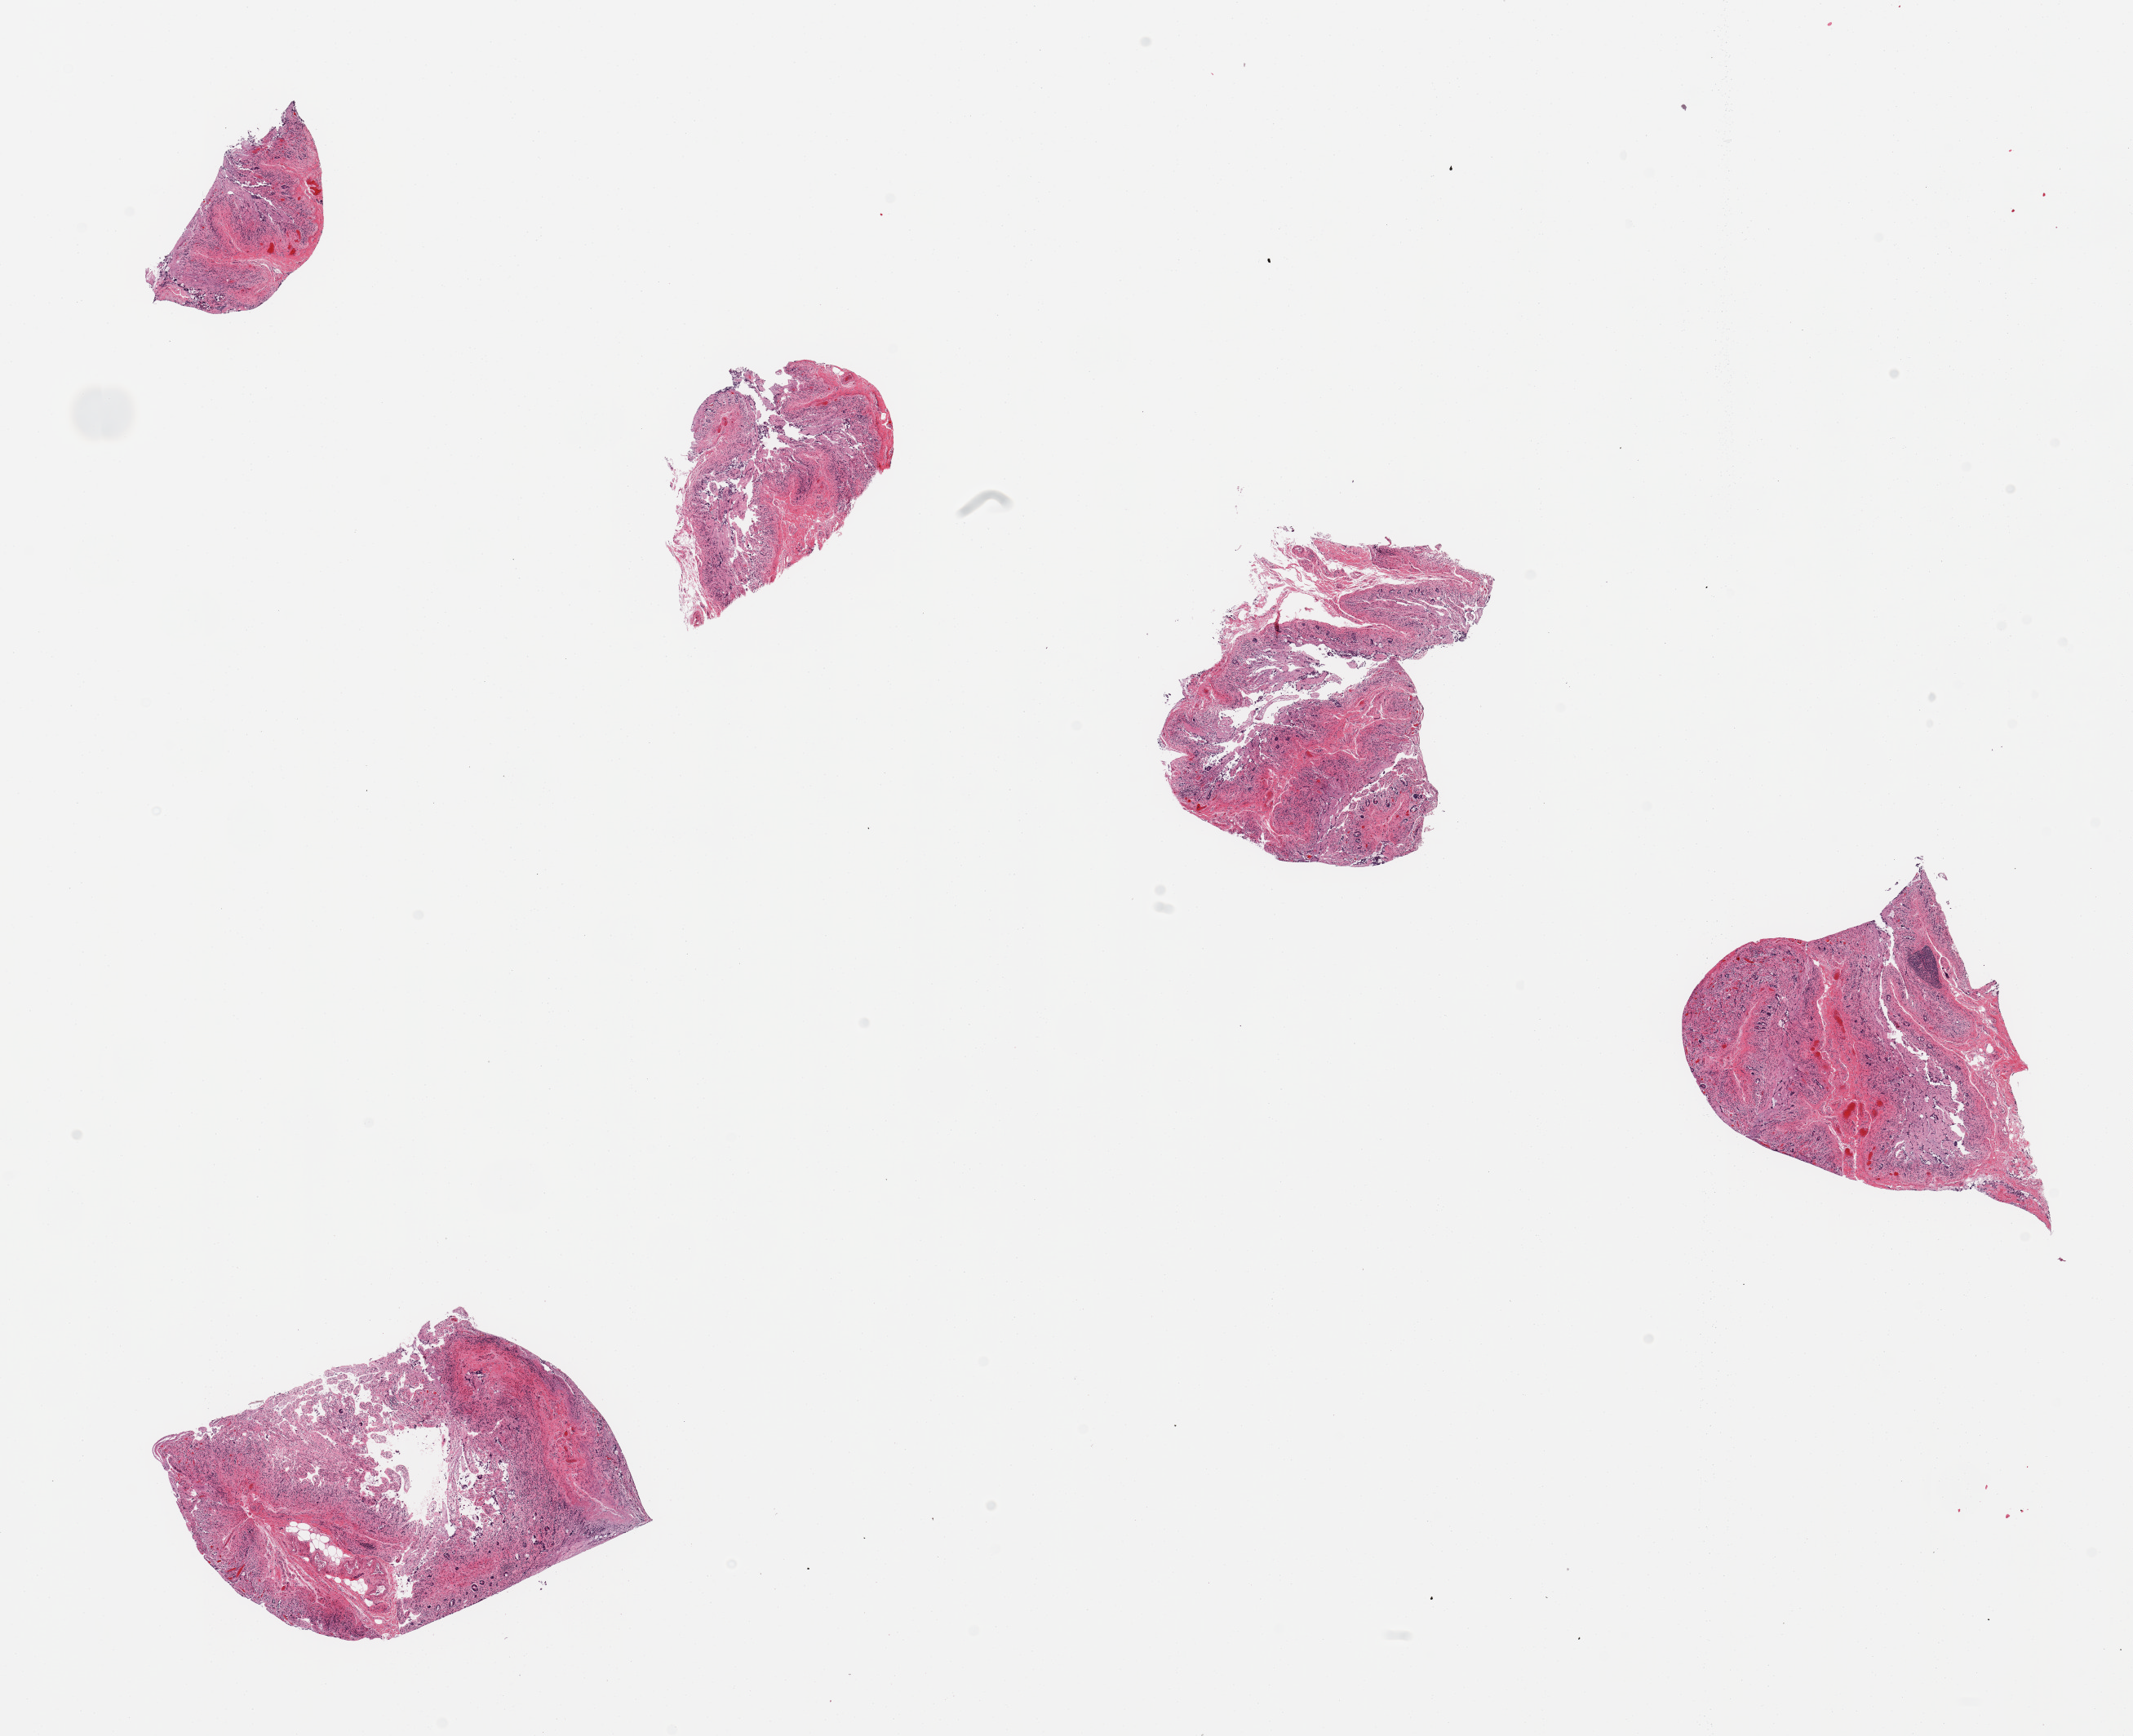
Hematoxylin and eosin (H&E) whole-slide image — whole scanned area (about 20.7 x 16.8 mm) shown as a low-resolution overview. PAXgene-fixed, paraffin-embedded tissue. Target tissue: ileum. Donor tissue sample. Male donor.
Pathologist's review note for this sample: 5 pieces; autolyzed and congested mucosa with one lymphoid nodule.